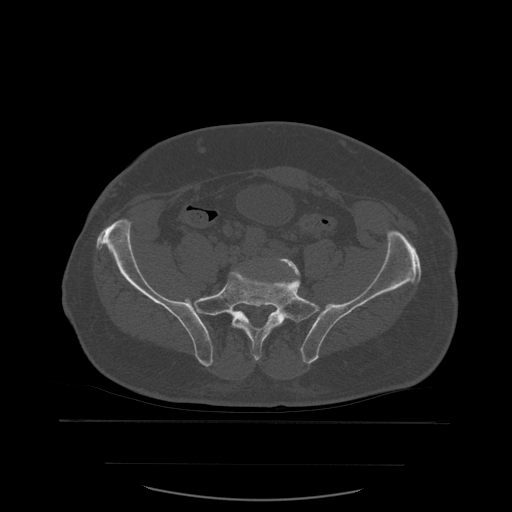
CT including the spine, one axial slice; slice 118 of 590 in the series (ordered by position); bone window (W 1800 / L 400 HU); 512 × 512 image matrix. Patient age 71 years. From the clinical record (not read from this slice): primary cancer: lung; vertebrae with lytic lesions (as recorded): T1, T2, L5, S1.
Outlined on this slice (semi-automatic segmentation, software-assisted and operator-edited):
- L5 vertebra: box from (x=253, y=258) to (x=301, y=357) px